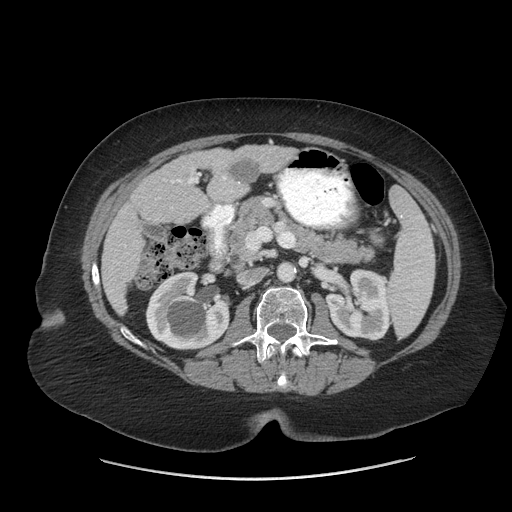
Contrast-enhanced abdominal CT (liver protocol), one axial slice; slice 23 of 69 in the series (ordered by position); reconstruction kernel STANDARD; 140 kVp; soft-tissue window (W 400 / L 40 HU); 2.5 mm slice thickness; 512 × 512 image matrix, field of view 420 × 420 mm. From the clinical record (not read from this slice): diagnosis: hepatocellular carcinoma (patient treated with transarterial chemoembolisation; whether this scan precedes or follows treatment is not stated here); TNM stage (as recorded): Stage-IIIB; Child-Pugh class: A; tumour differentiation: moderately differentiated.
Annotated regions visible in this slice (semi-automatically segmented with operator editing):
- liver parenchyma outside the tumour (the mass and vessels are separate outlines, so this box may not span the whole liver): bounding box (x1, y1, x2, y2) in pixels: (102, 144, 296, 314)
- liver vessels: (171, 176, 226, 184)